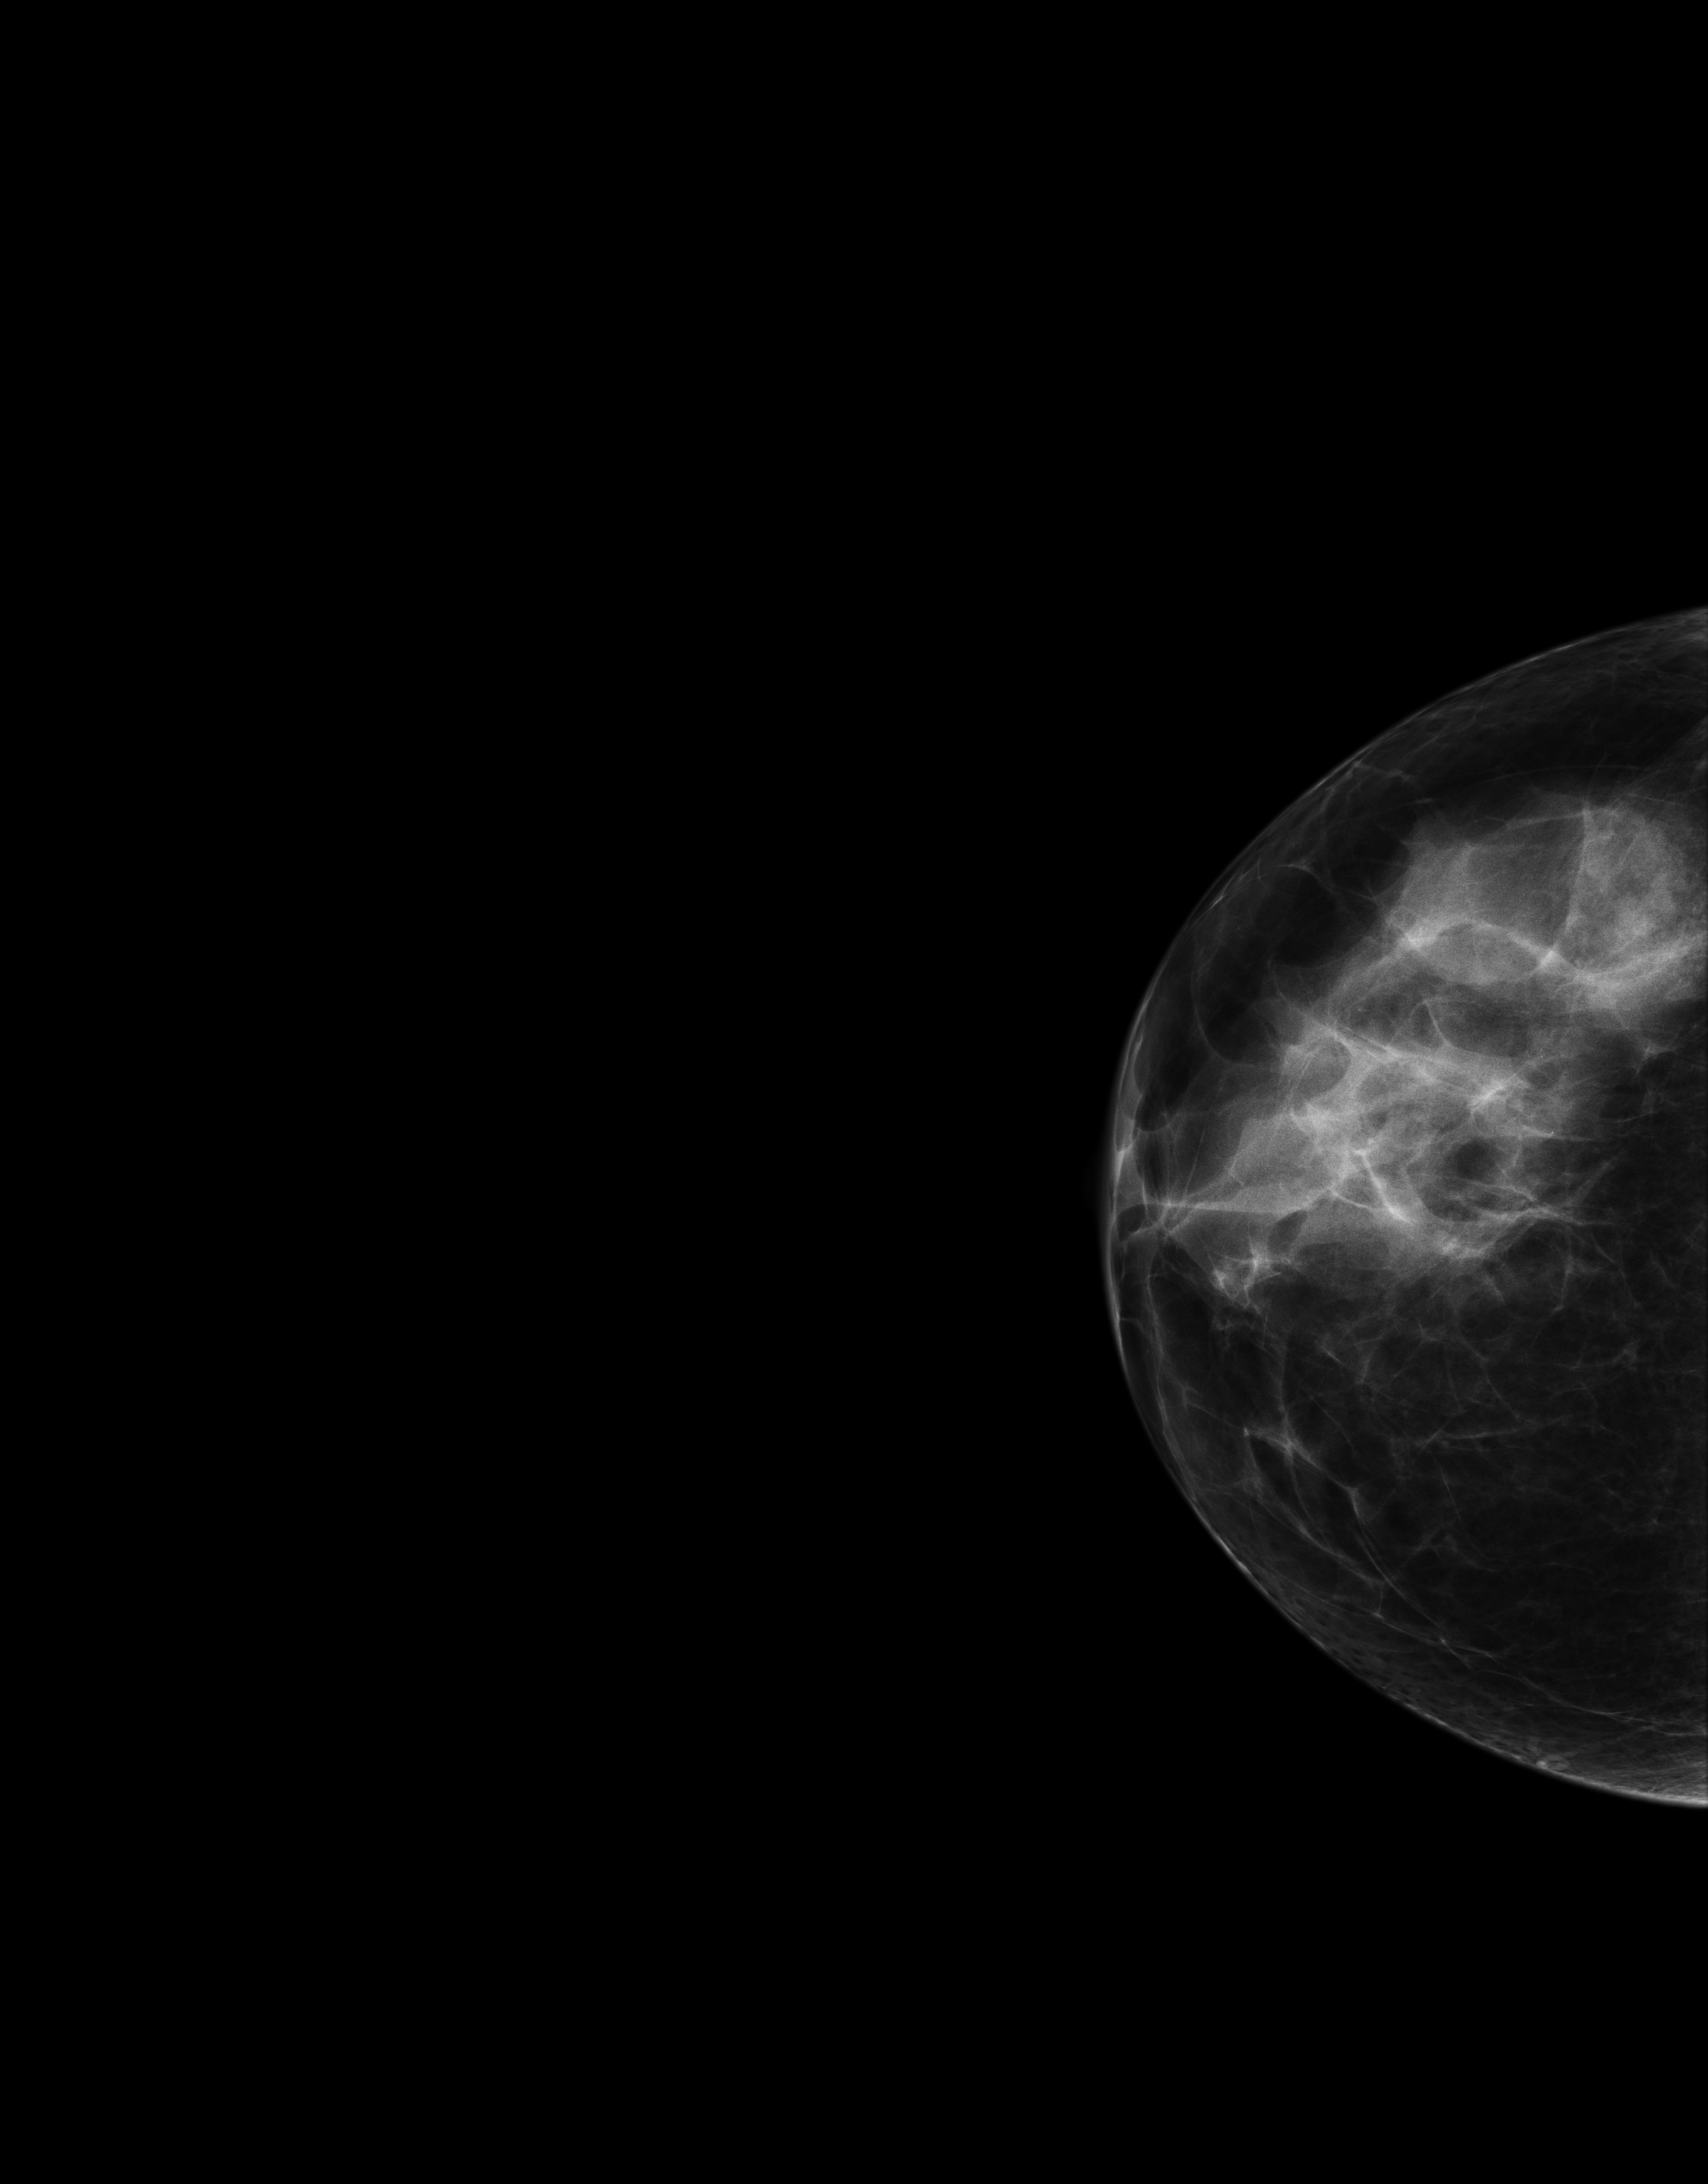
Full-field digital mammogram (FFDM), right breast, cranio-caudal projection, annual screening mammography examination. Patient: female, 51 years.
Breast density at the screening exam (both breasts): heterogeneously dense (BI-RADS density category c). Final BI-RADS assessment for this screening round (tomosynthesis exam, both breasts): category 1. Recall: no recall after this screen.